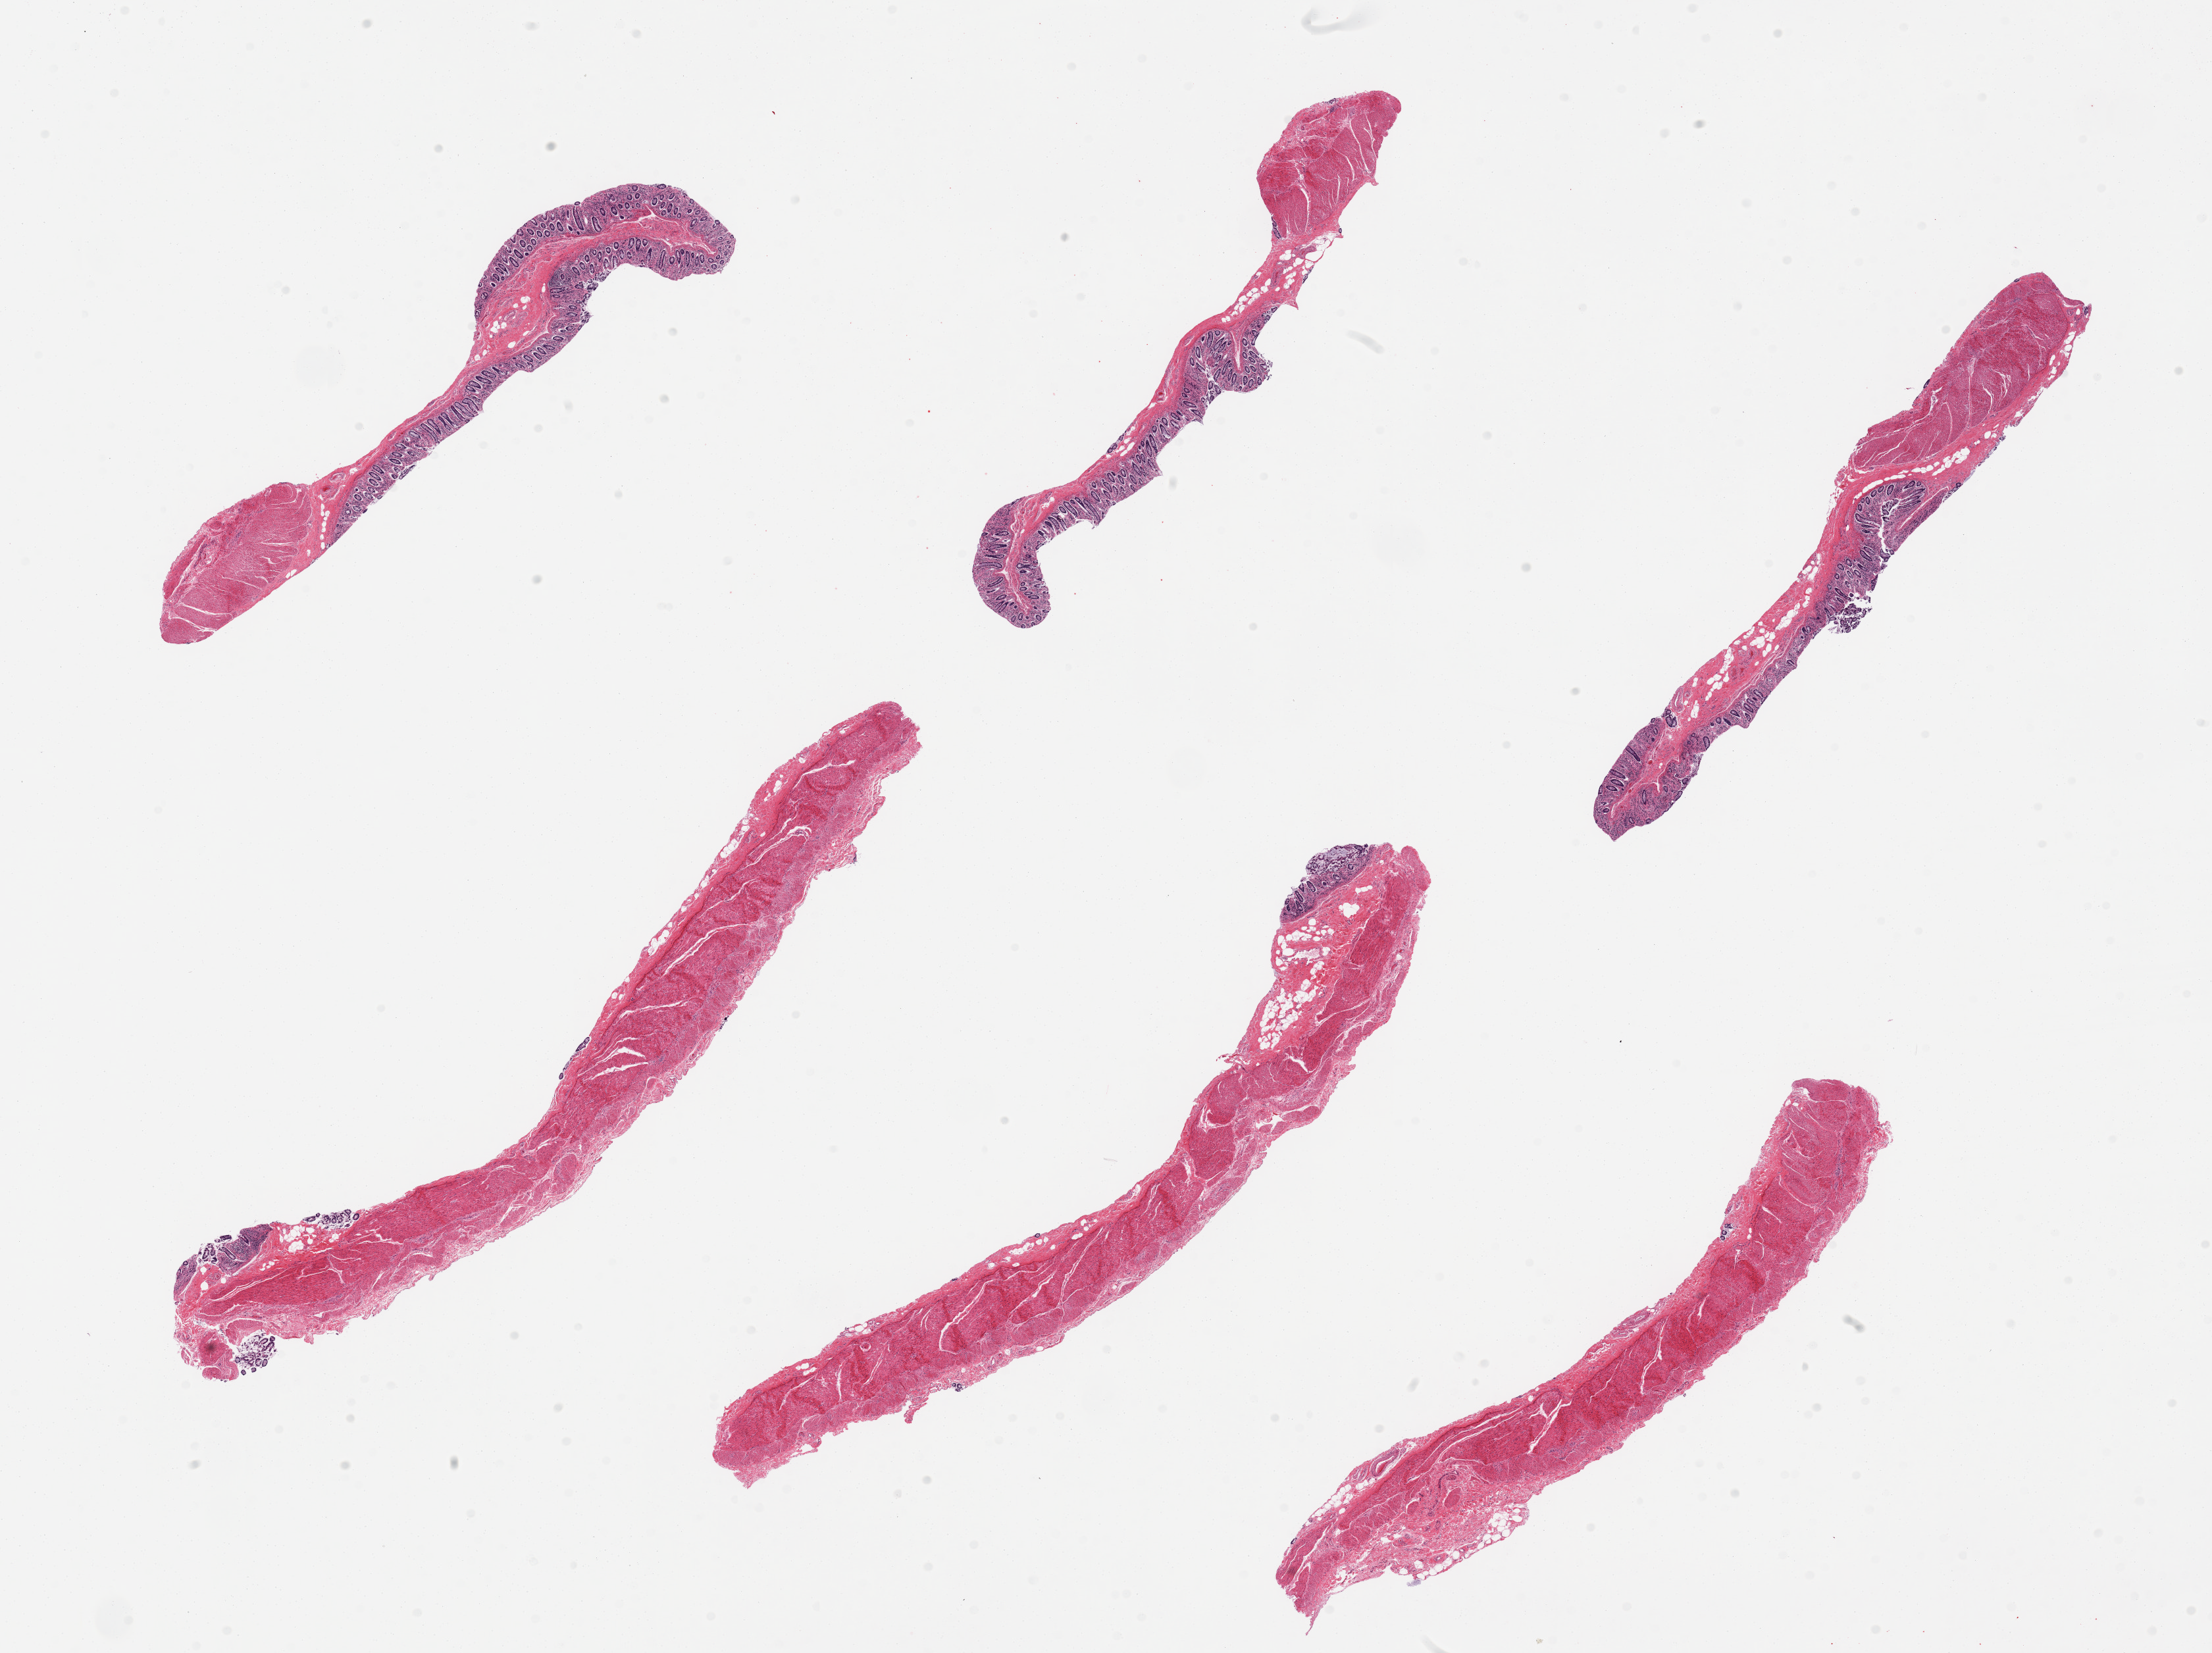
Whole-slide image, haematoxylin and eosin stain, brightfield, shown as a low-resolution overview of the whole scanned area (about 26.6 x 19.9 mm, from a 20x scan). PAXgene-fixed paraffin-embedded (PFPE) section. Target tissue: transverse colon. Donor tissue sample. Donor: male.
Reviewer comment on this tissue sample: 6 pieces; 3 with minimal mucosa.